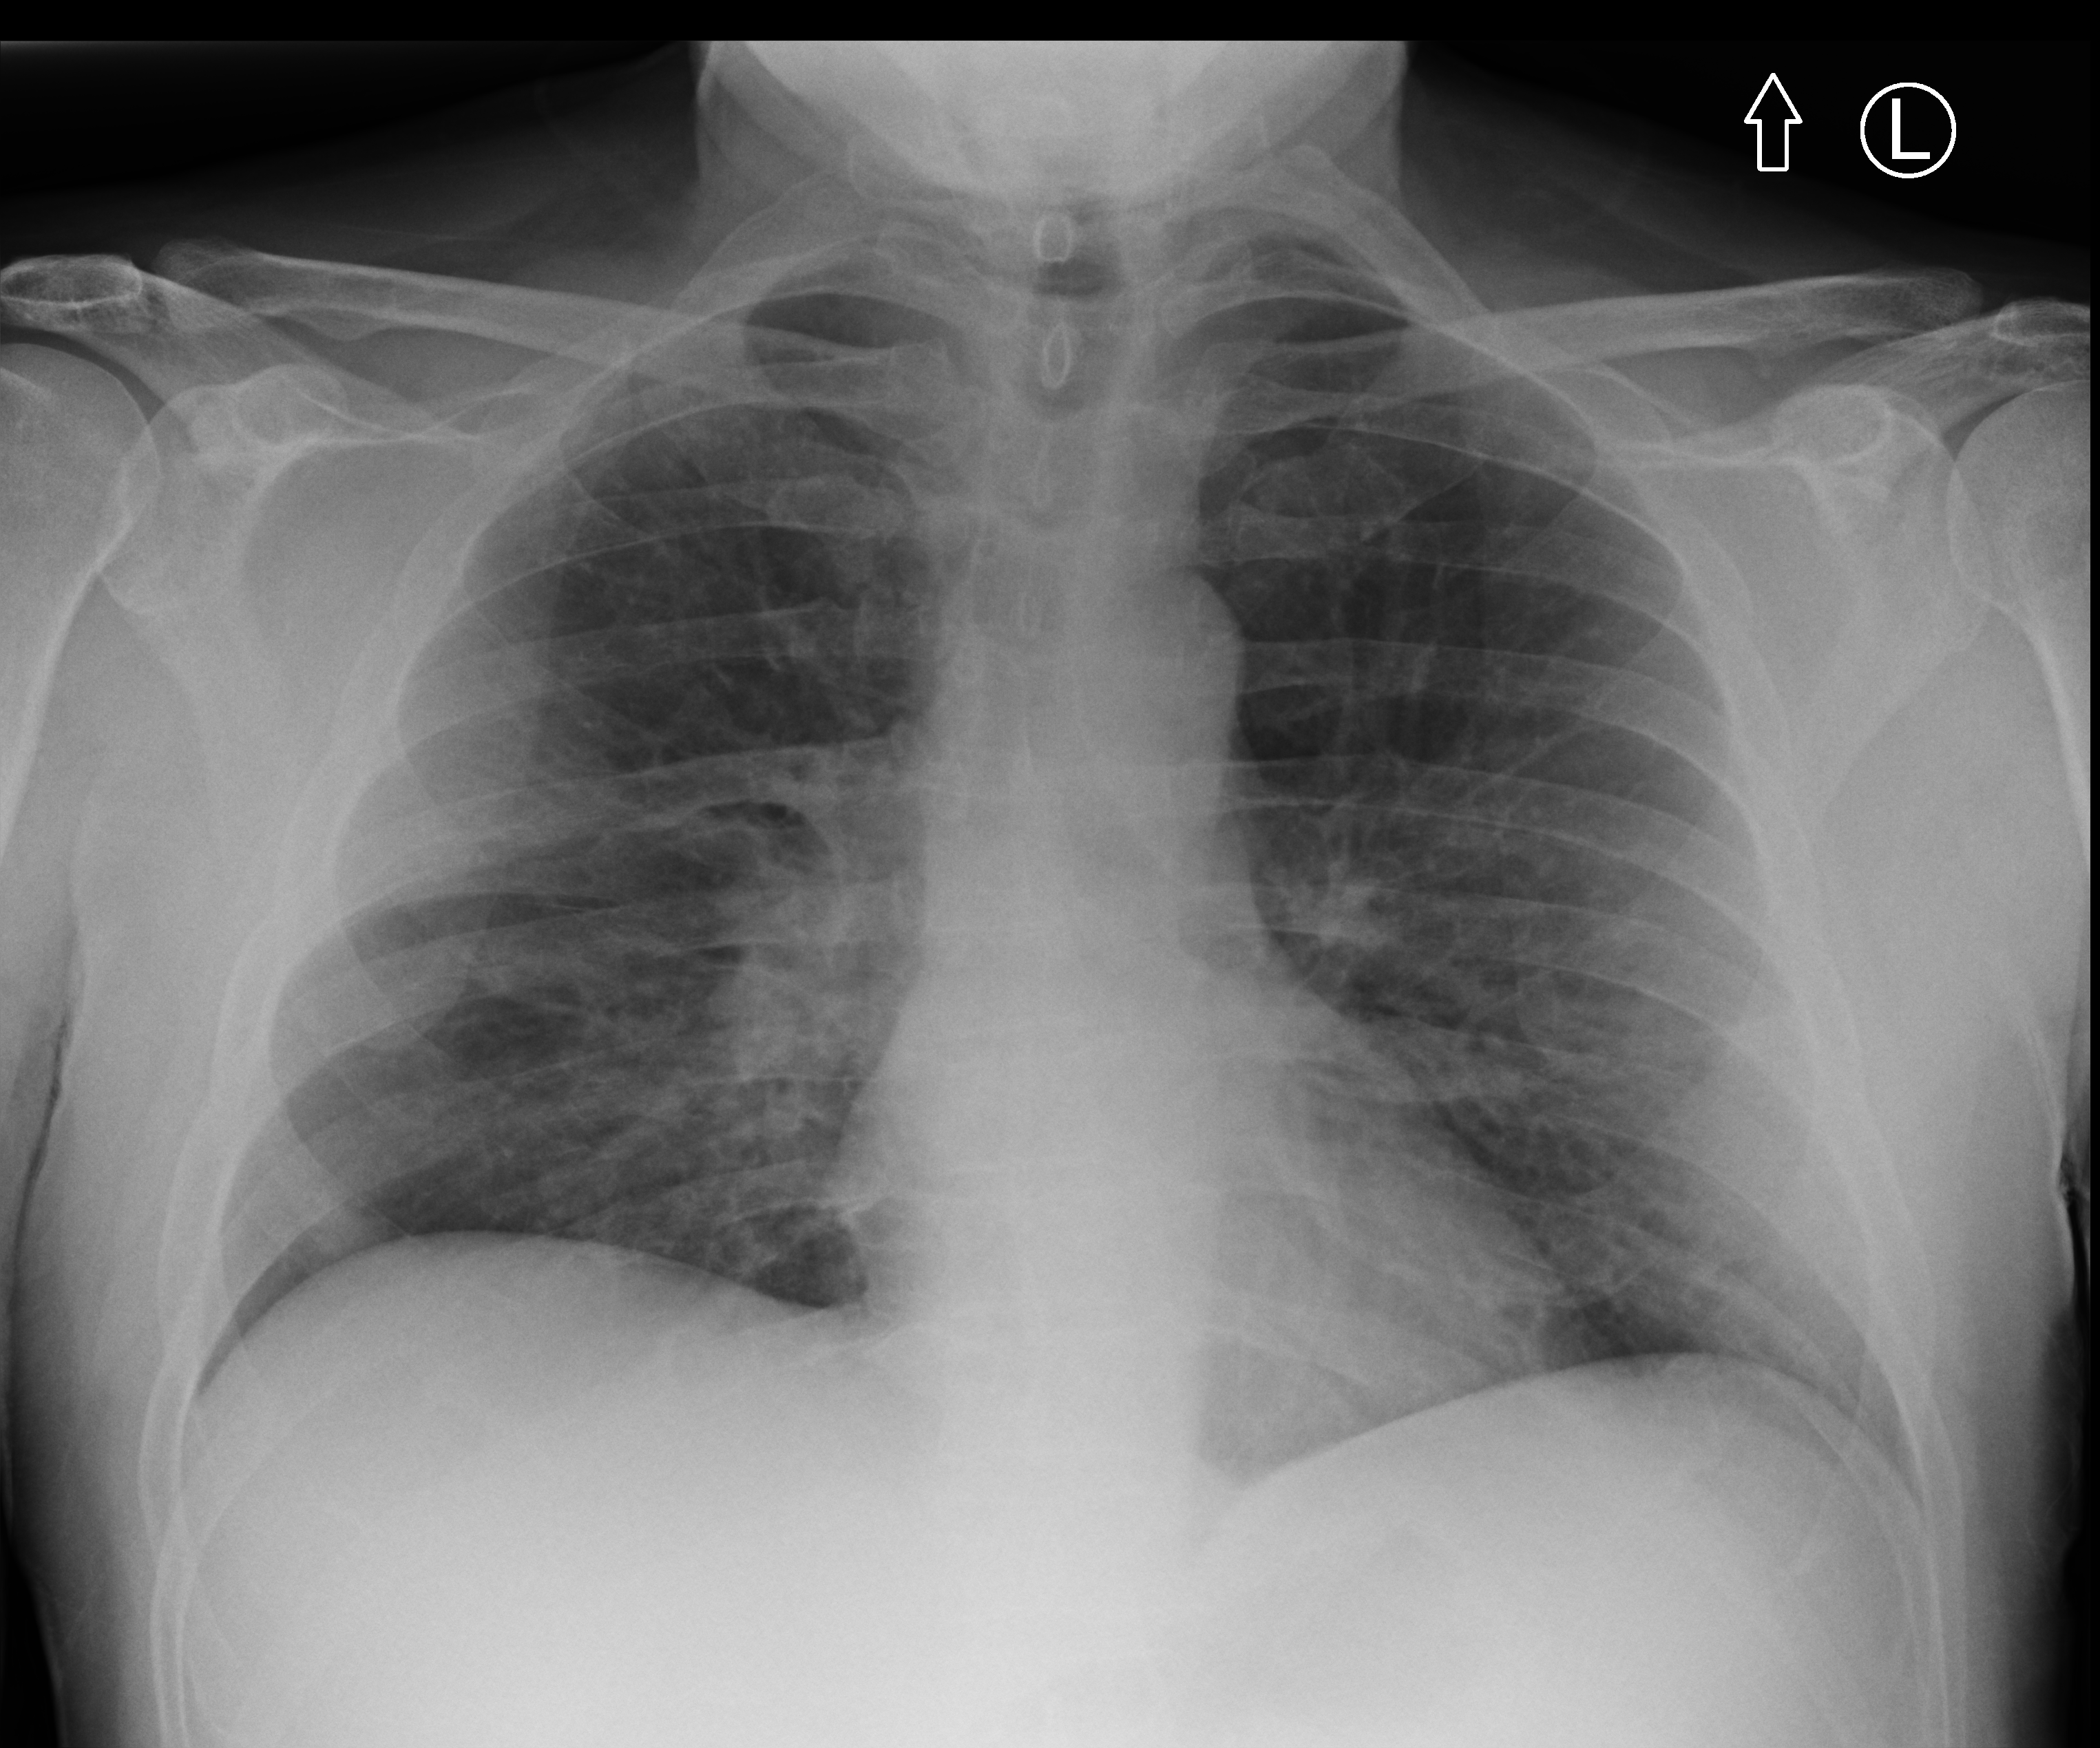
Portable chest radiograph, anteroposterior (AP) projection. Patient hospitalised with COVID-19; male, aged 18–59 years.
From the hospital-stay record, not from the radiograph (when in the stay this image was taken is not recorded): other chronic lung disease (admission record): no; mechanically ventilated during this hospital stay: no.